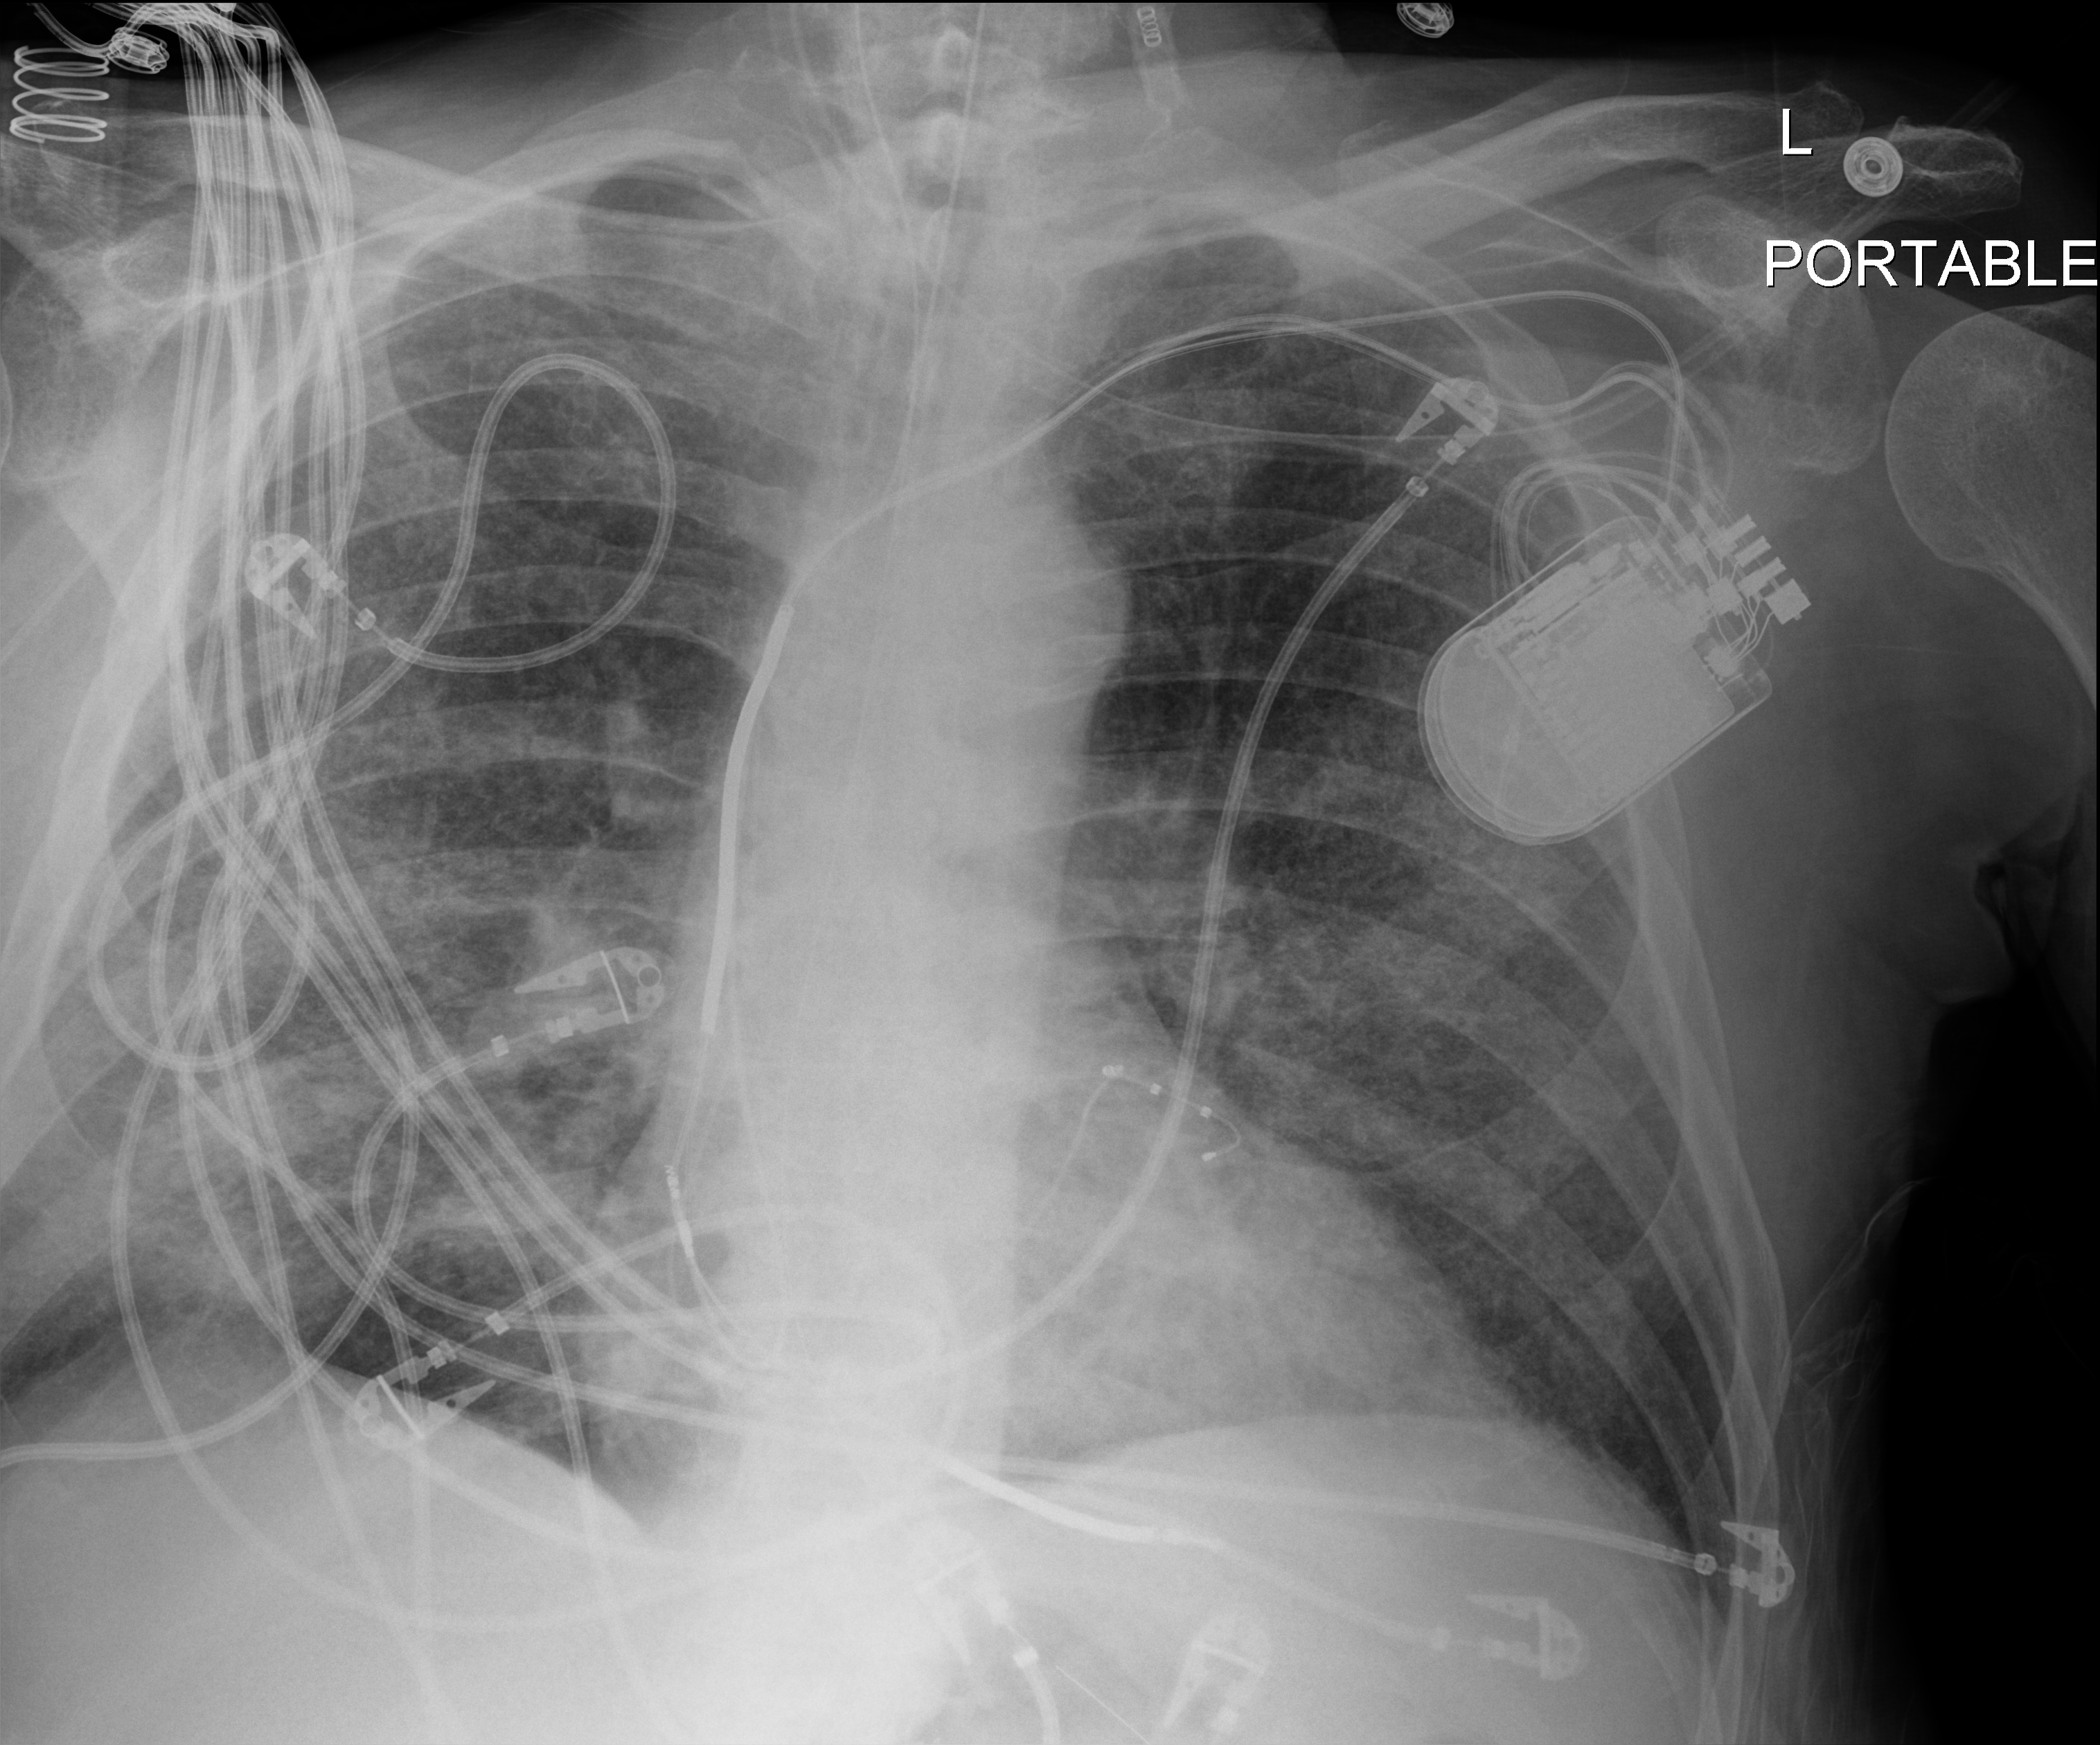
Chest X-ray (portable). Patient hospitalised with COVID-19; male, aged 60–74 years.
Hospital-stay facts (about this admission, not read from this image; timing relative to this image not recorded): mechanically ventilated during this hospital stay: yes; hypertension (admission record): yes; admitted to intensive care during this hospital stay: yes.